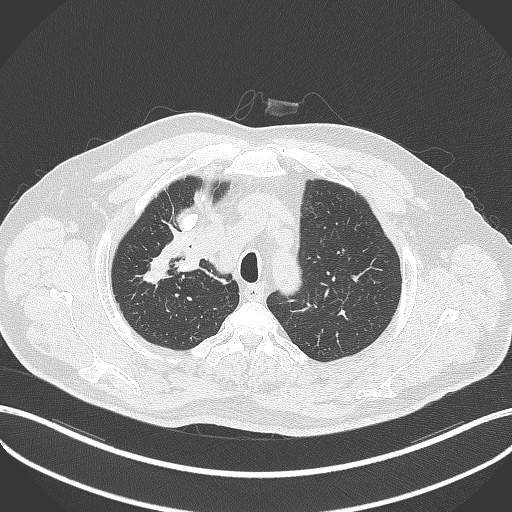
Chest CT, one axial slice. Slice 316 of 411 in the series (ordered by position). Reconstruction kernel B70f. 120 kVp. Lung window (W 1500 / L -600 HU). 1 mm slice thickness. 512 × 512 image matrix. Patient: male, 60 years. From the clinical record (not read from this slice): clinical TNM (as recorded): T1b N1 M0.
Annotated regions visible in this slice (bounding box drawn by a radiologist):
- lung tumour (recorded histology: squamous cell carcinoma): bounding box [x1, y1, x2, y2] px = [175, 233, 205, 275]